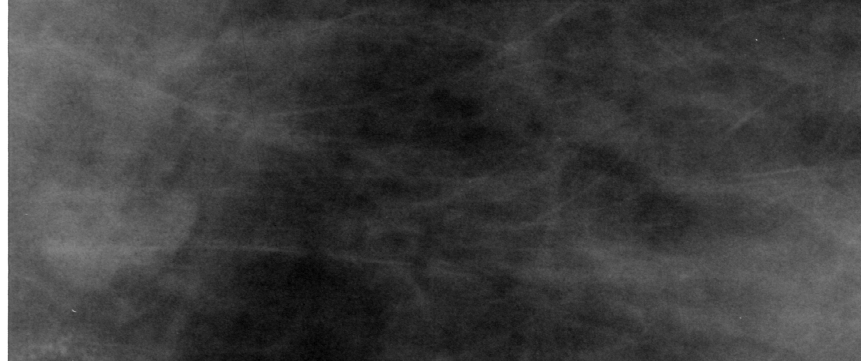
Crop from a digitized film mammogram around one marked abnormality, left breast, MLO view, BI-RADS breast density category 3 (scale 1–4).
Finding: calcifications, morphology vascular; BI-RADS assessment category 2; benign without callback (not worked up further).